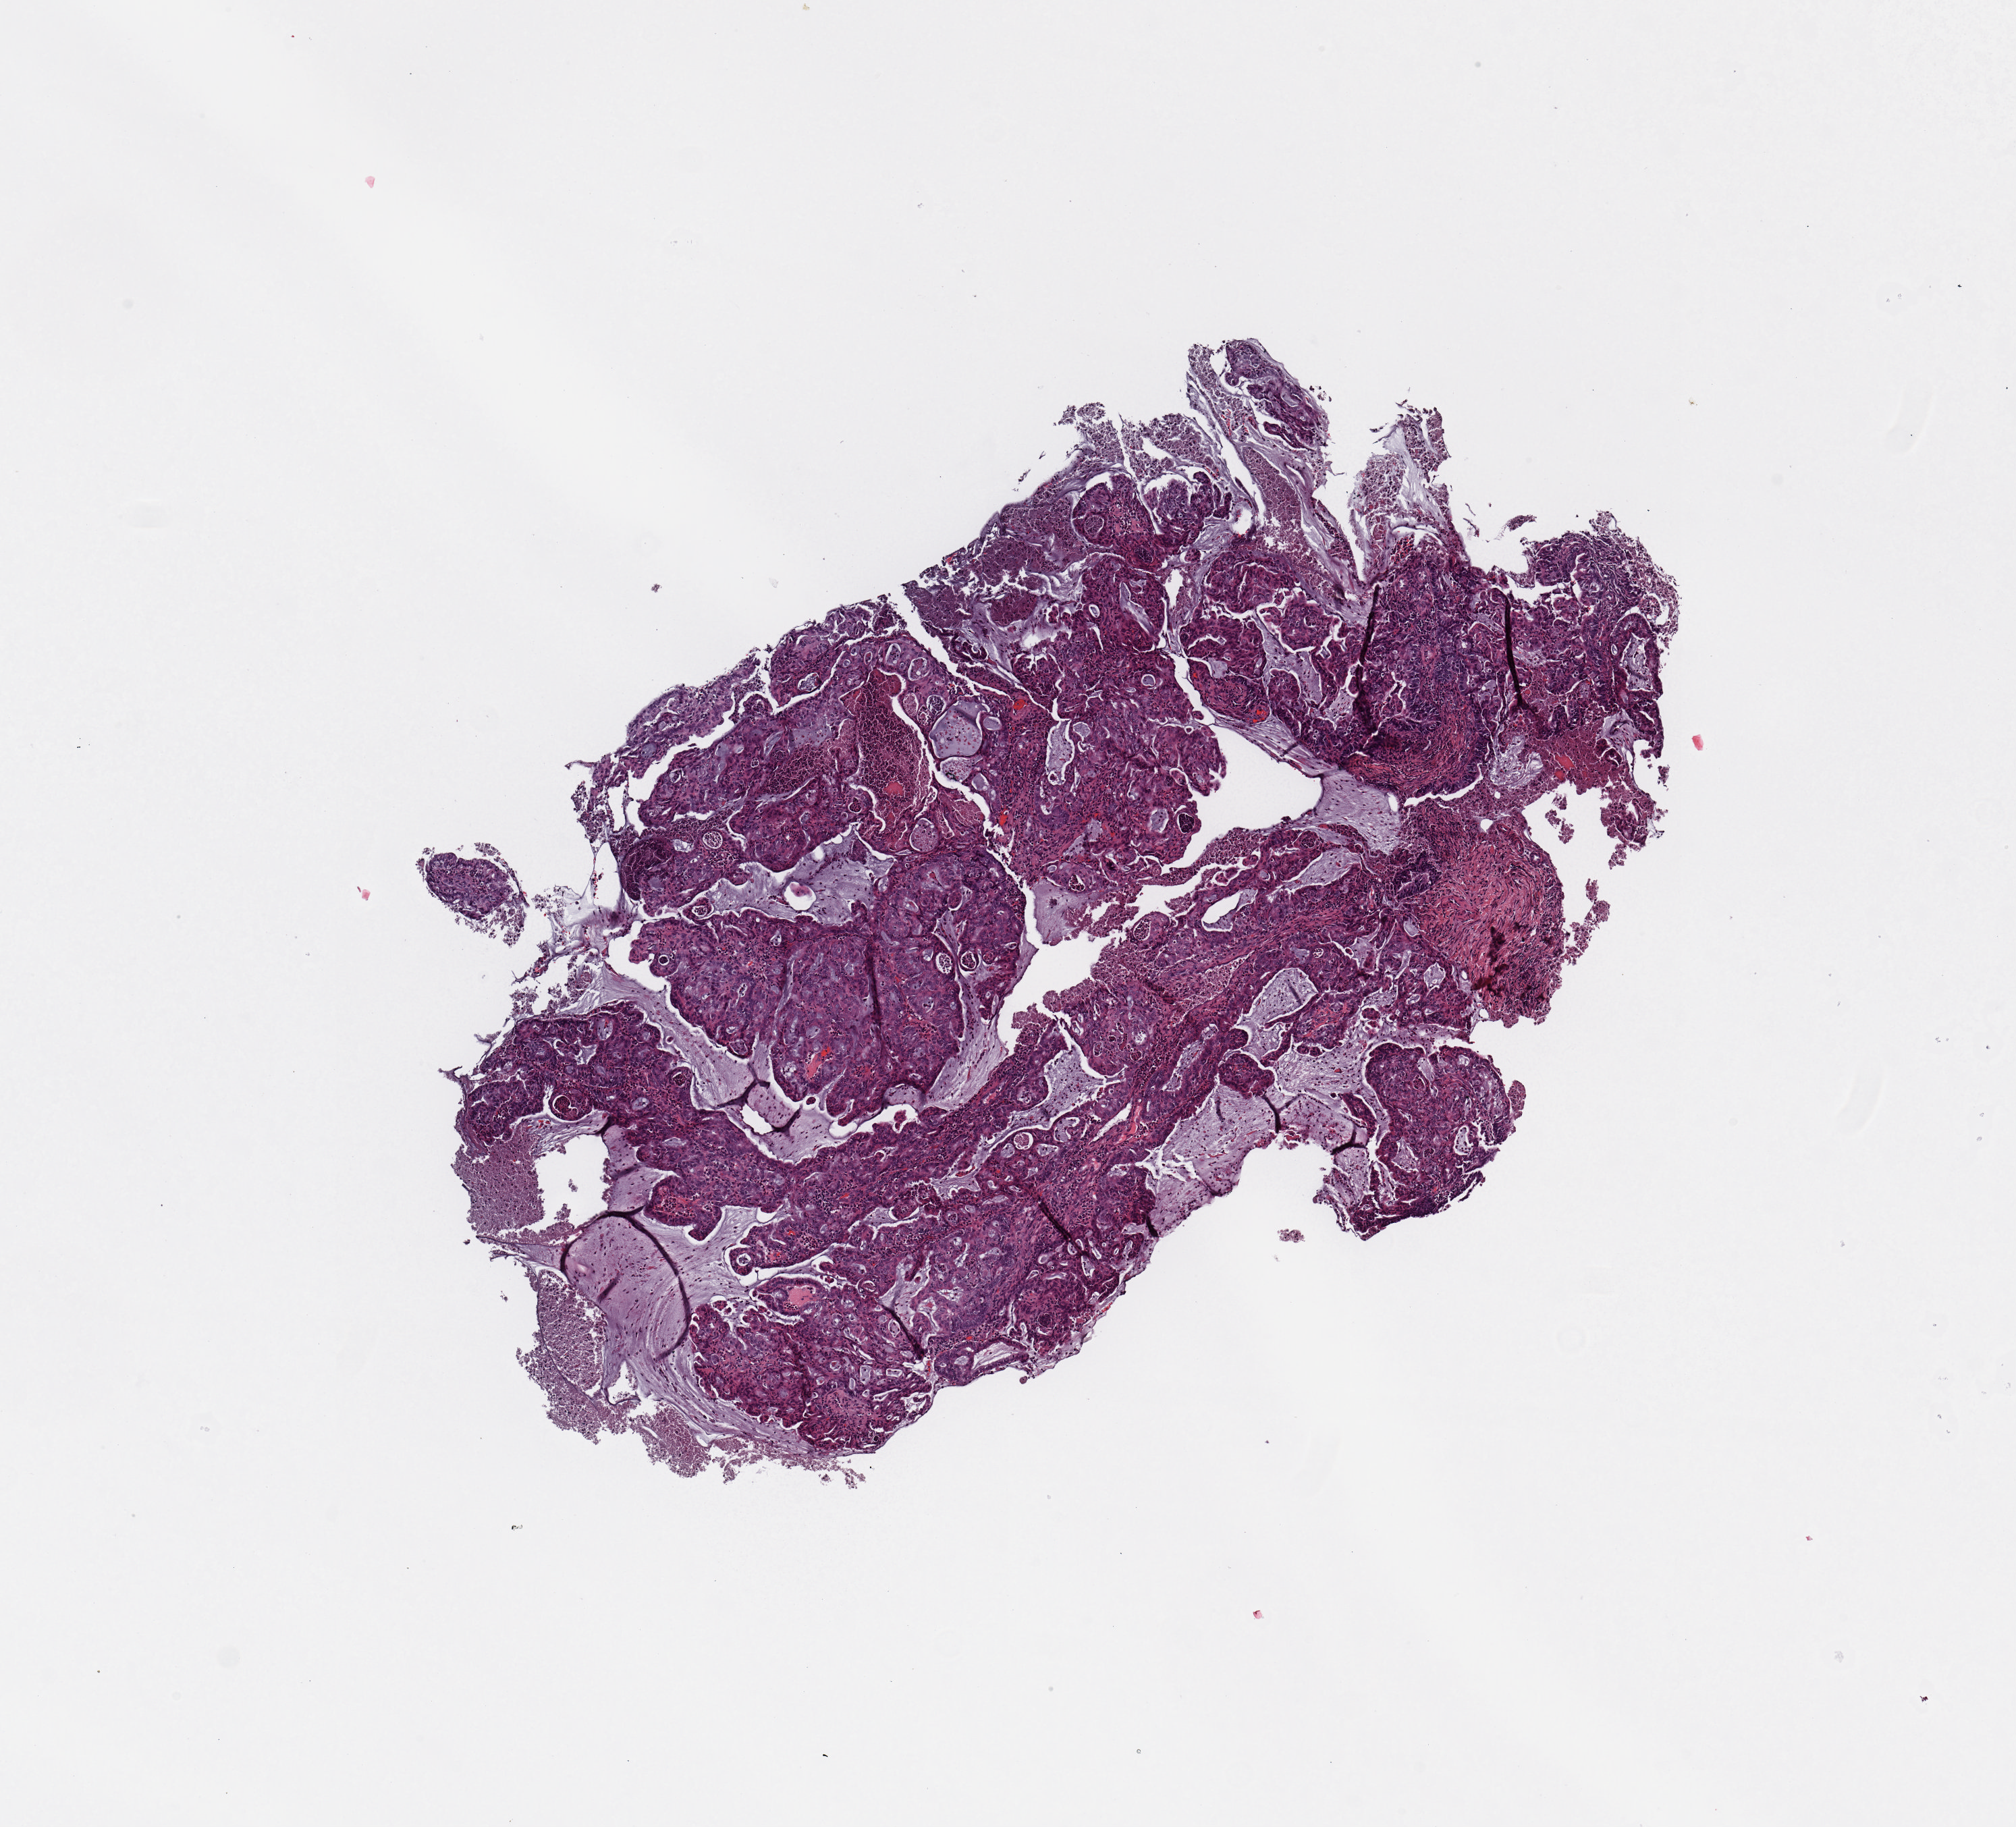
H&E-stained whole-slide image — shown as a low-resolution overview of the whole scanned area (about 5.9 x 5.4 mm, slide scanned at 20x), tumour tissue sample, sampled site: uterus. Female, 69 y/o. Histologic grade: G2 (moderately differentiated). Pathologist review of this section (percent, as recorded): tumour nuclei 80%, necrosis 15%.
- diagnosis: Endometrioid adenocarcinoma, NOS
- AJCC pathologic stage: IA